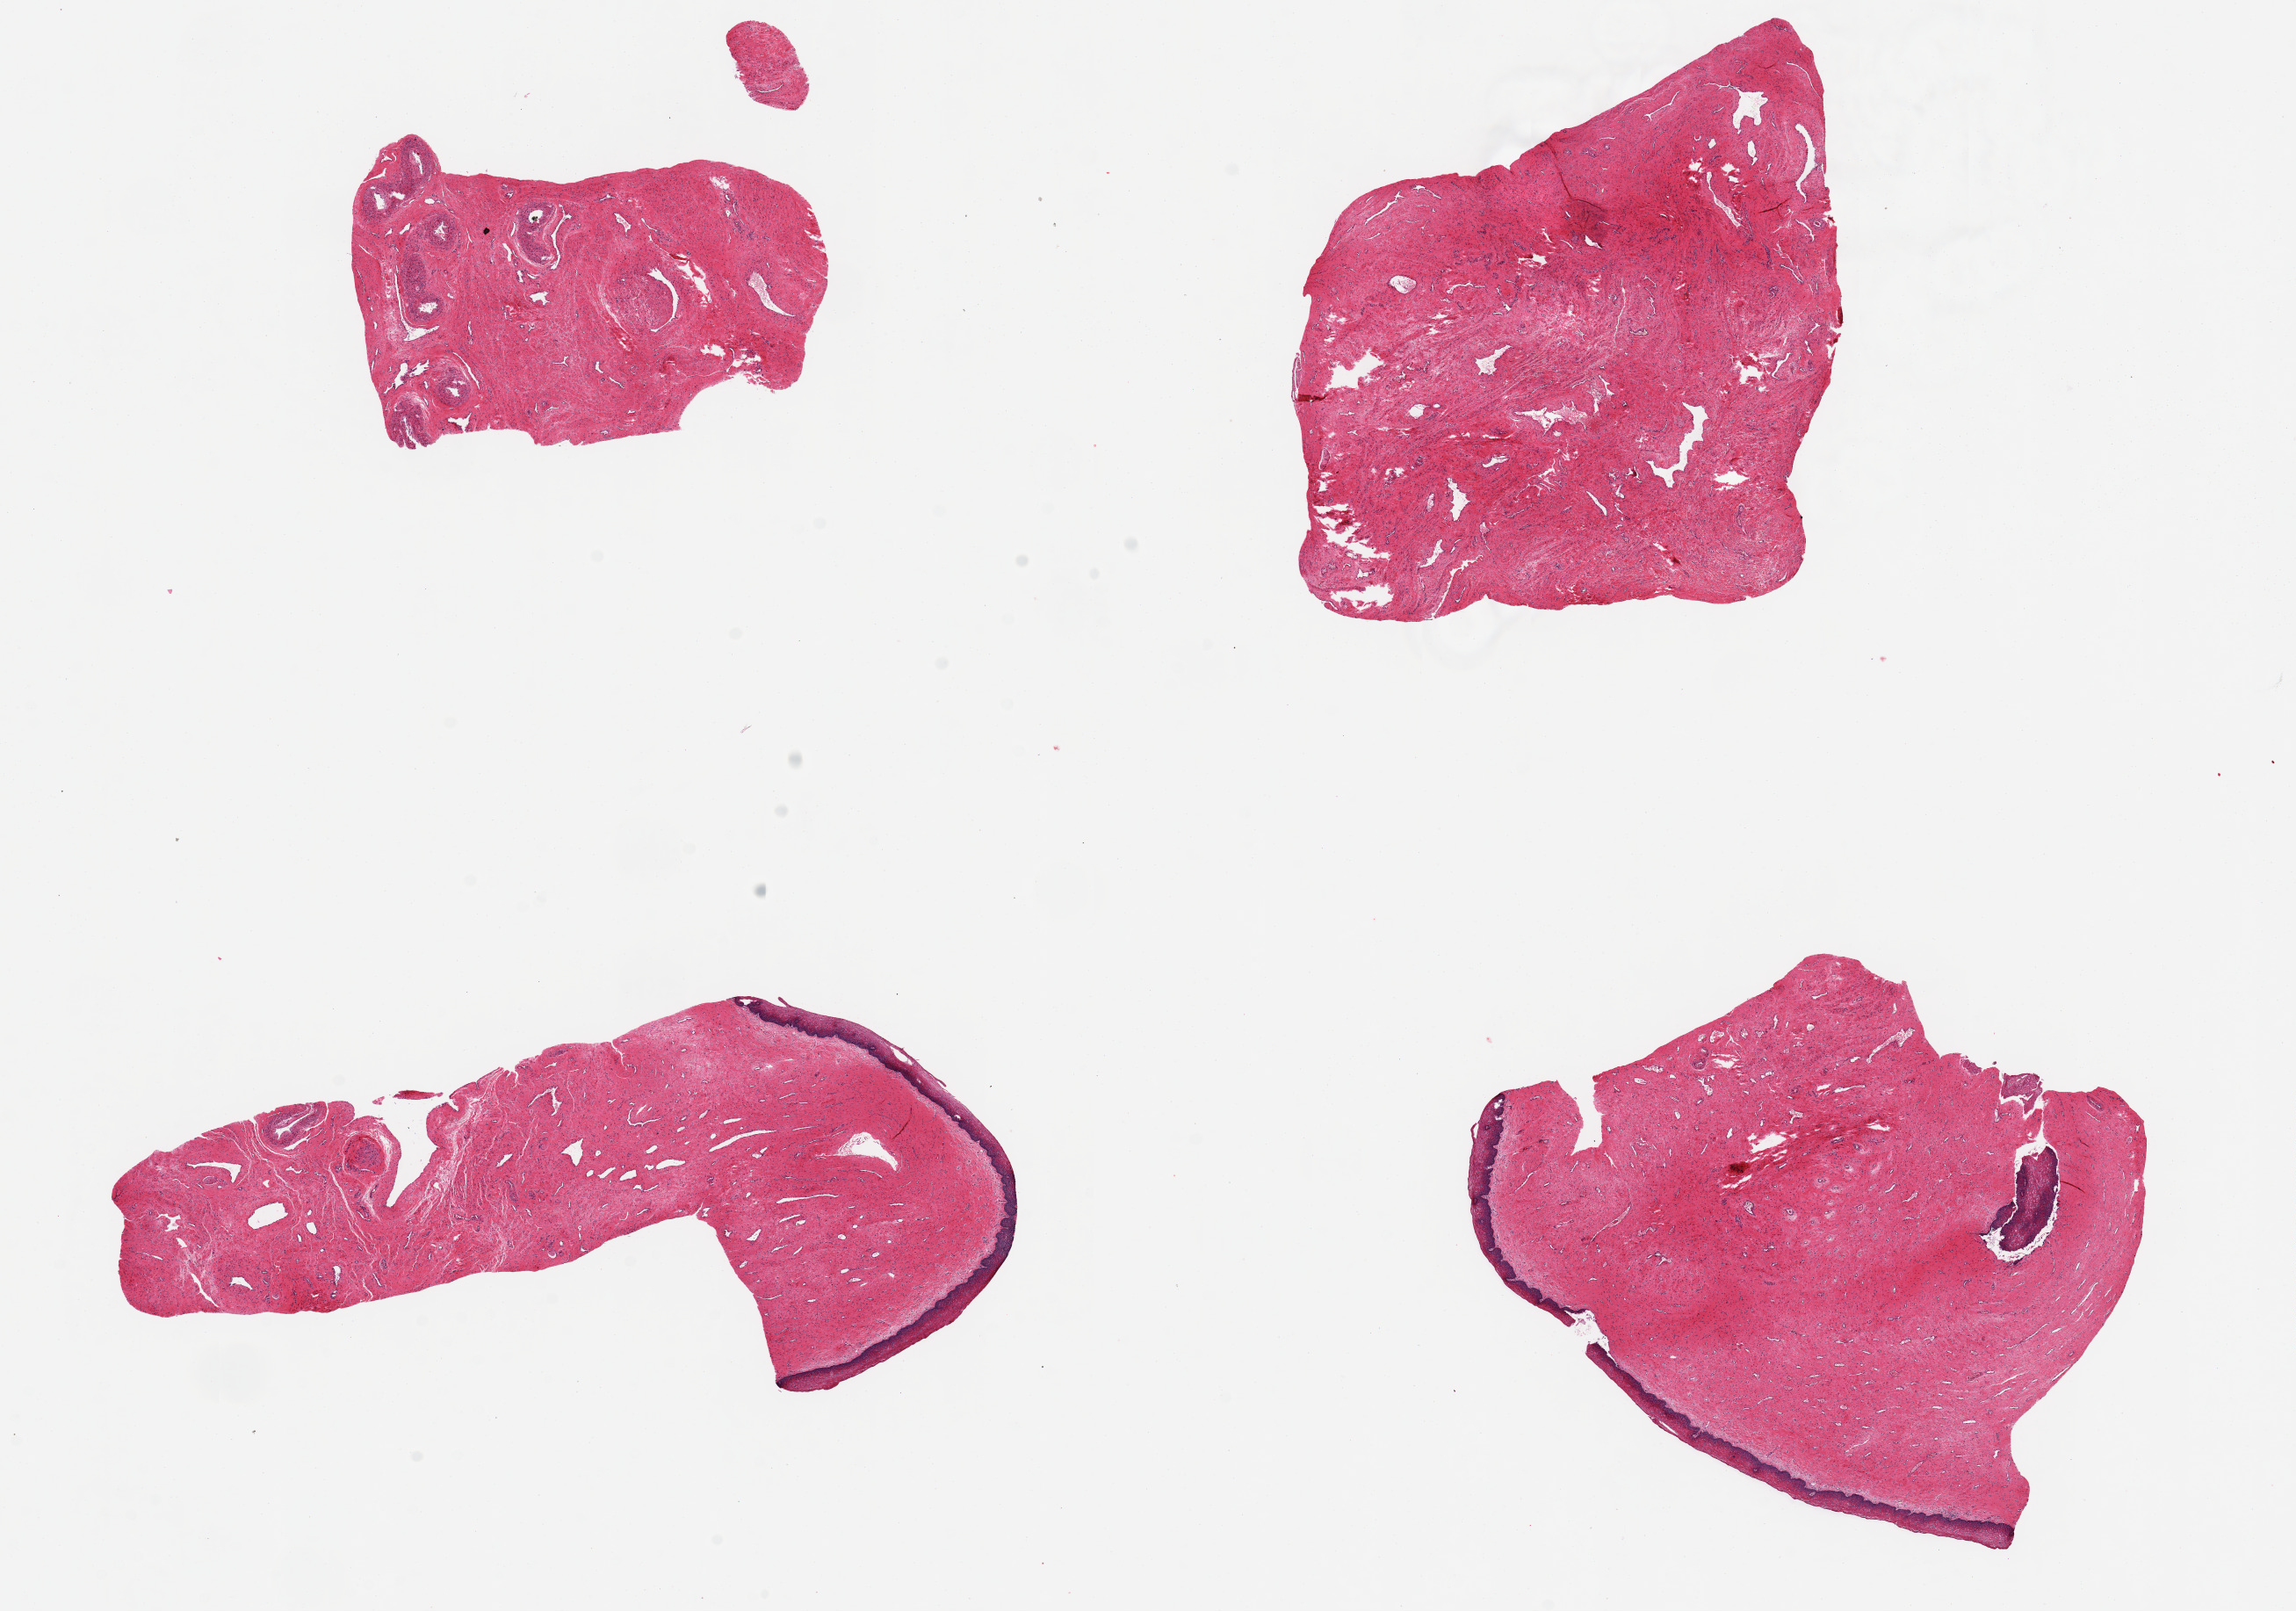
Haematoxylin and eosin whole-slide image — a low-resolution overview of the entire scanned area, about 20.7 x 14.5 mm (acquisition: 20x scan). PAXgene-fixed, paraffin-embedded tissue. Target tissue: exocervix. Donor tissue sample. Donor: female.
* reviewer comment on this tissue sample: 4 aliquots, ~6x4mm. Squamous mucosa present on 2 of 4 pieces, ~5% of thickness. No dysplasia evident